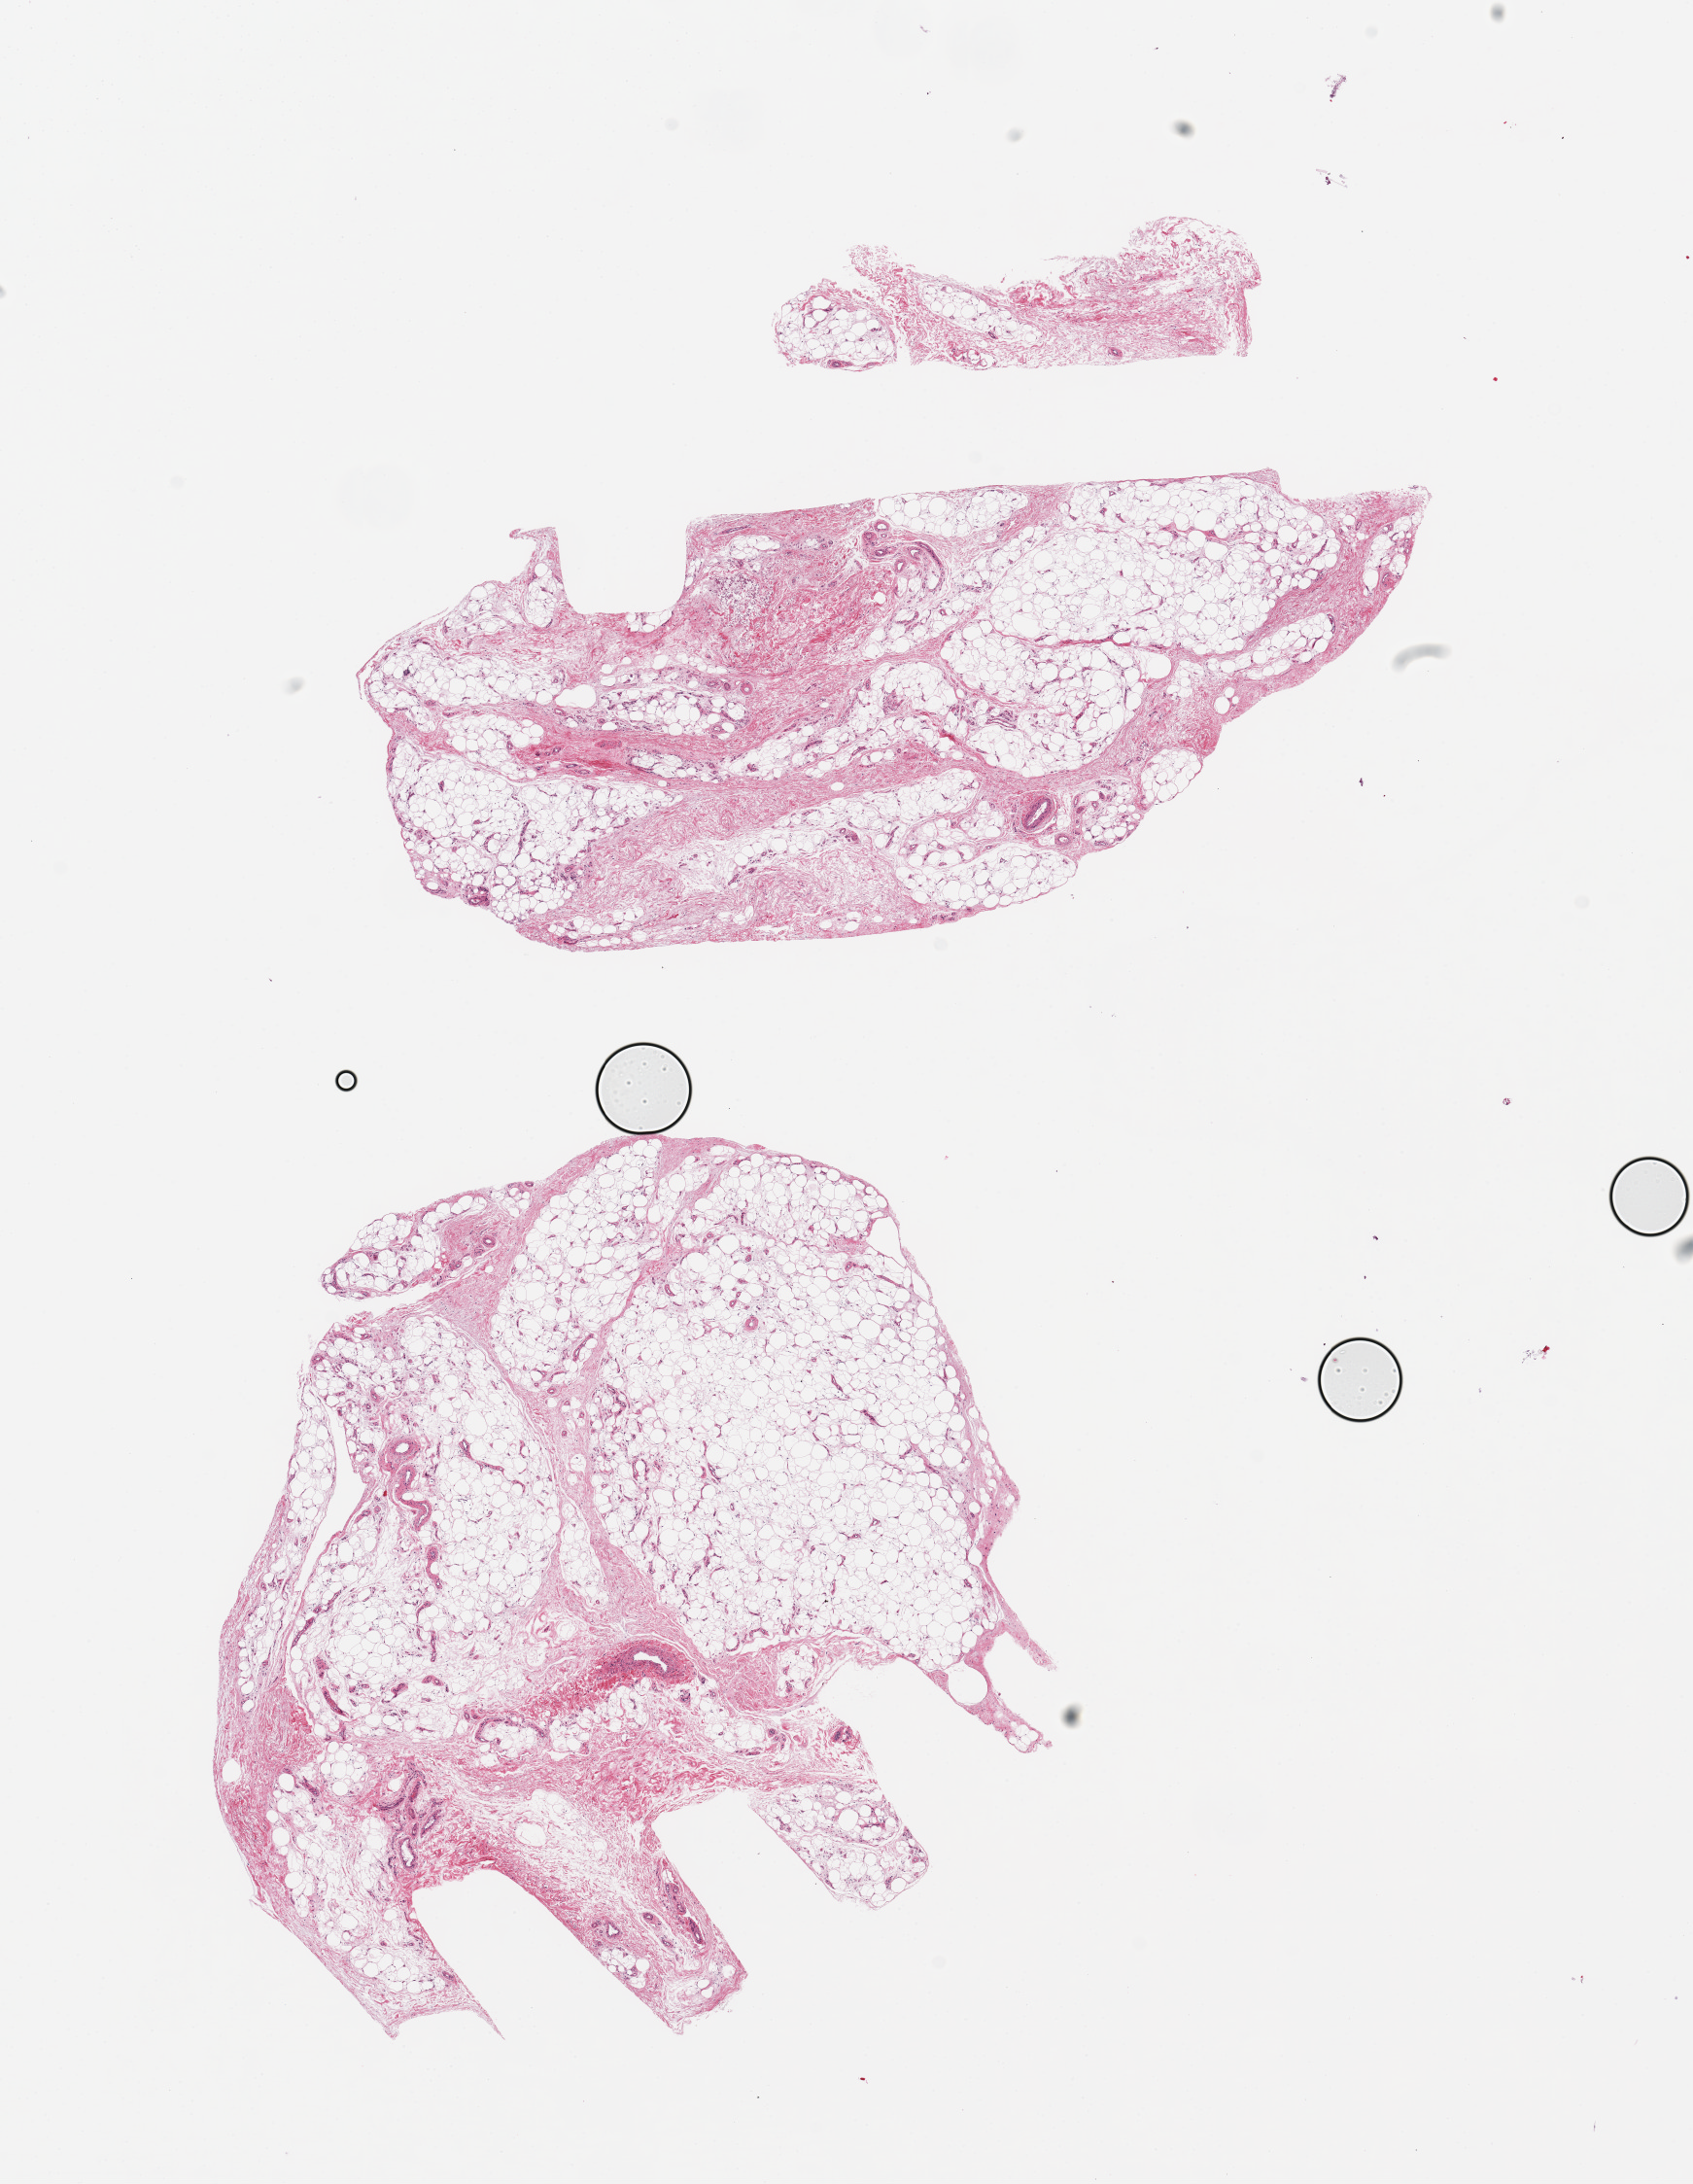
Hematoxylin and eosin (H&E) whole-slide image, brightfield — whole scanned area (about 13.8 x 17.8 mm) shown as a low-resolution overview. PAXgene-fixed paraffin-embedded (PFPE) section. Section of adipose tissue (target tissue). Tissue donor sample. Donor: female.
- reviewer comment on this tissue sample: 2 pieces, 8x4 & 7x6.5mm; smaller piece has more fibrous stroma than larger